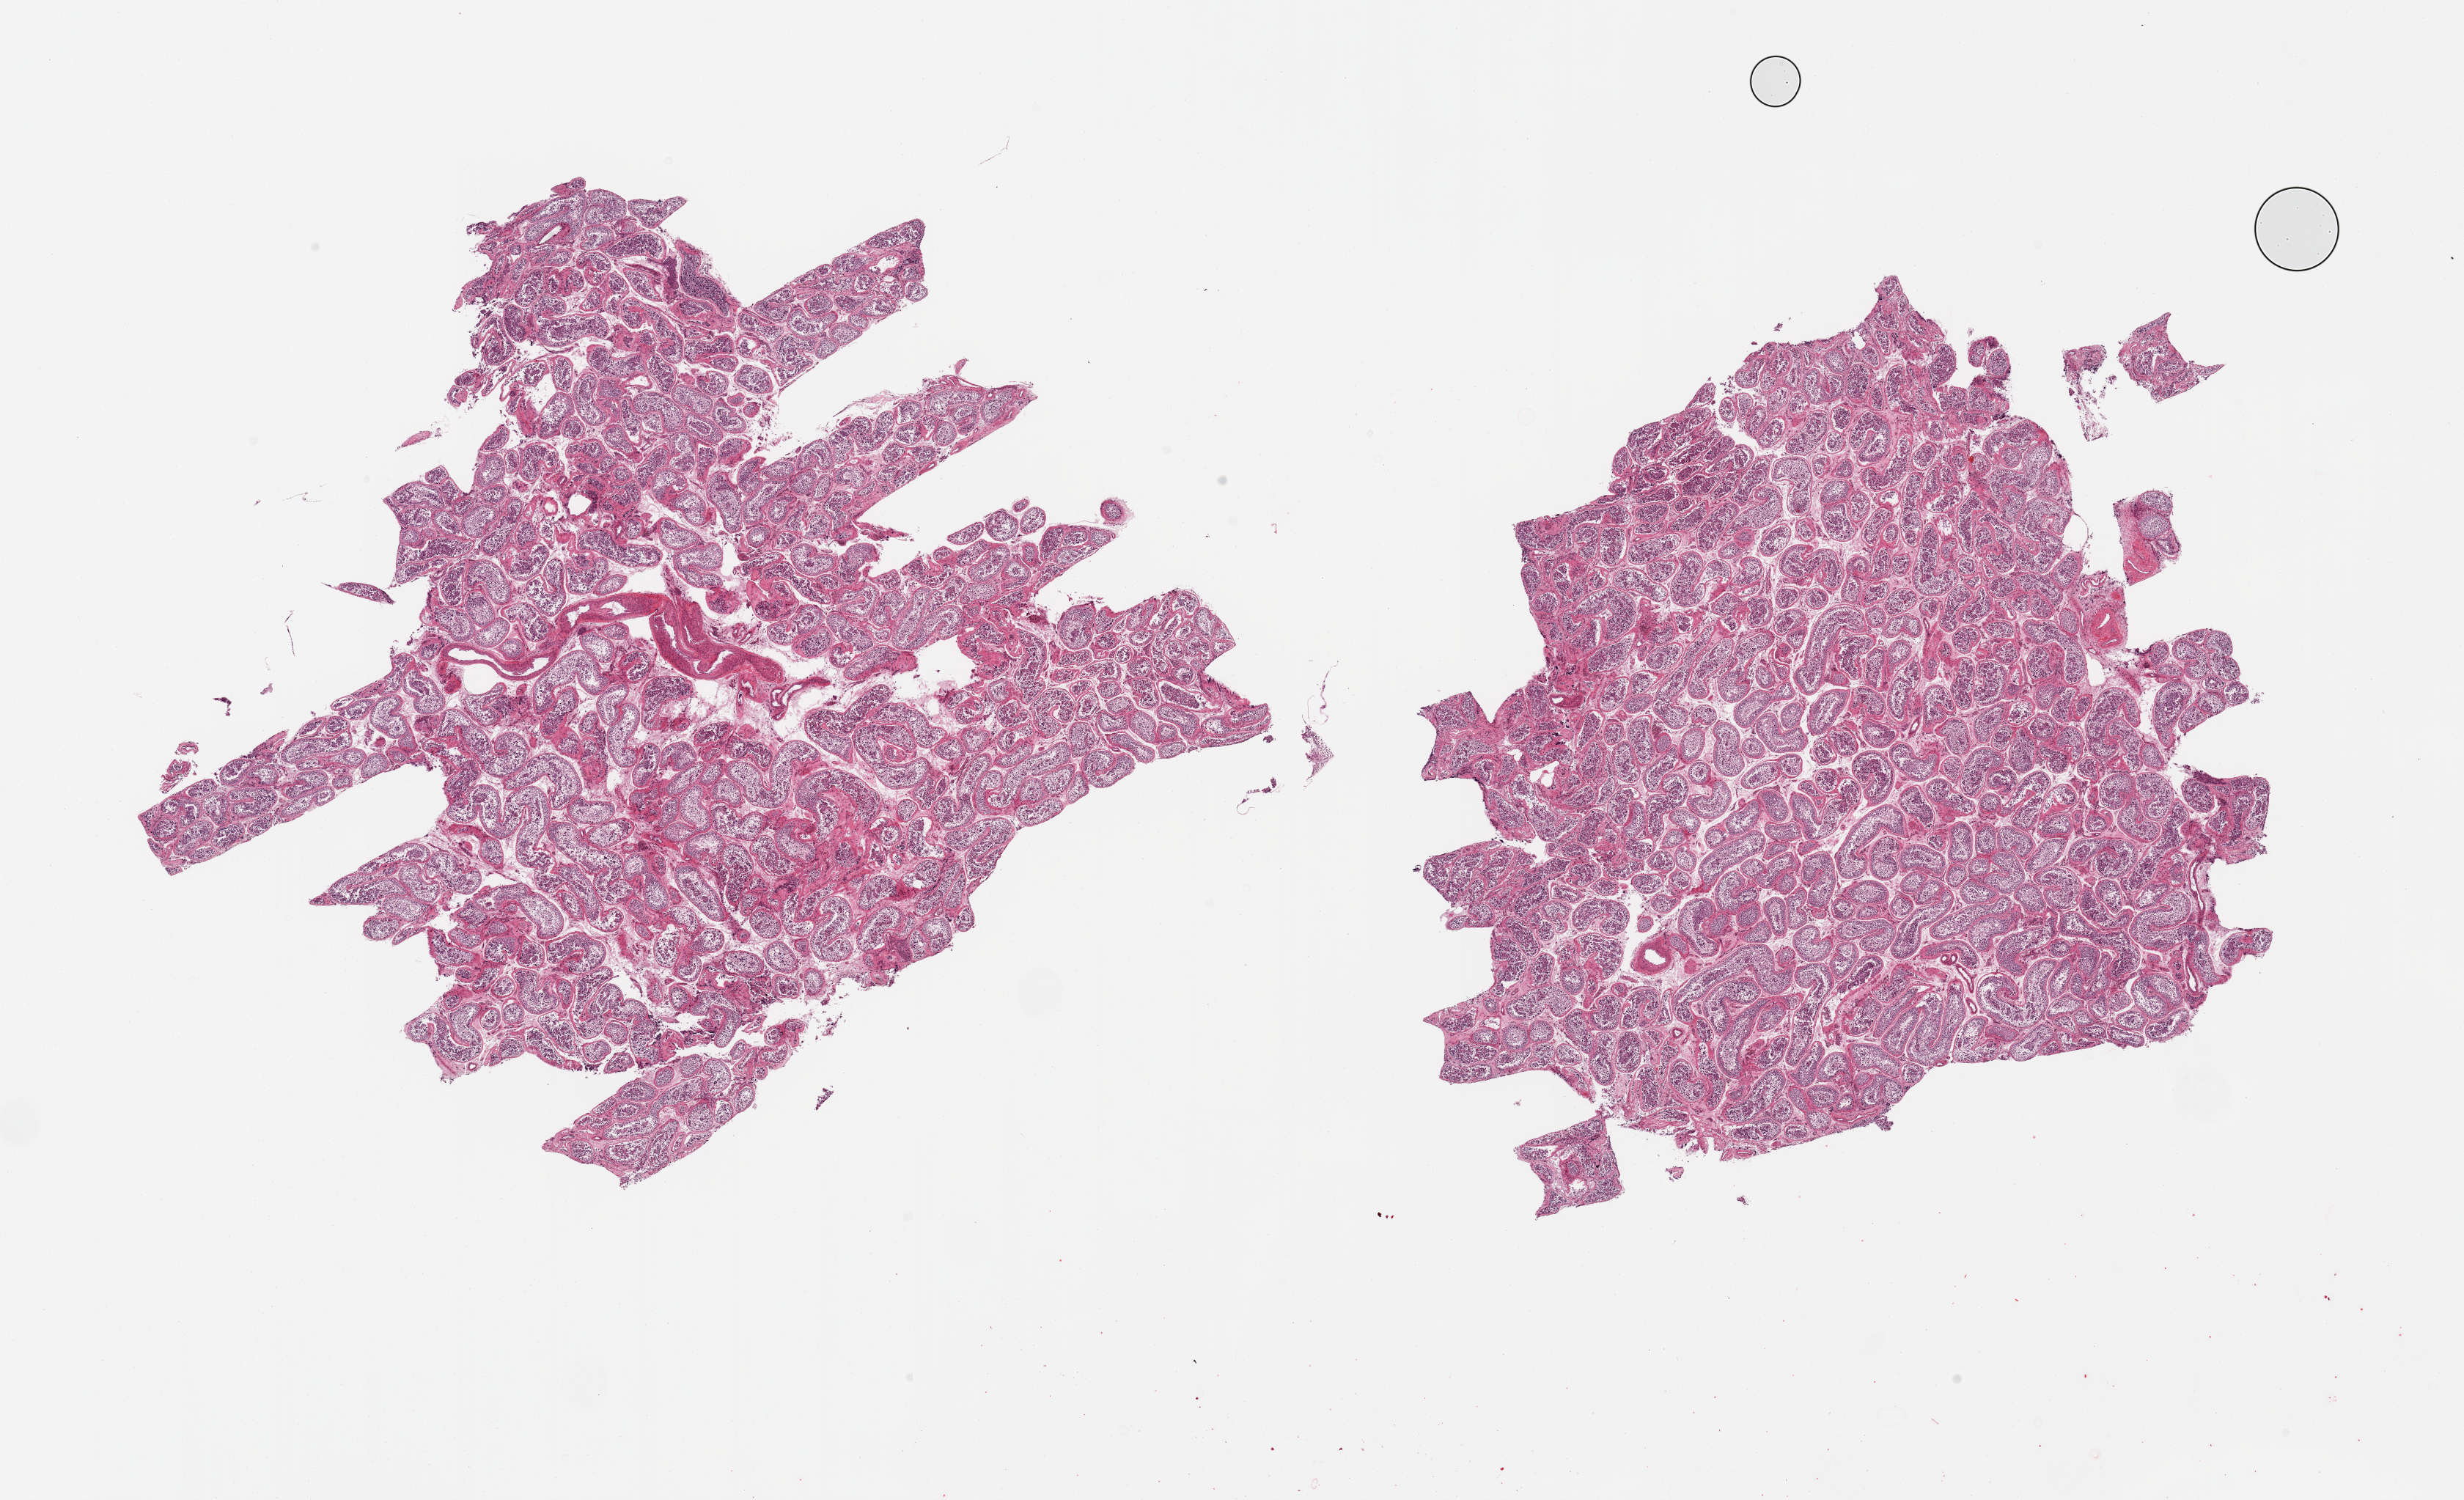
Hematoxylin and eosin (H&E) whole-slide image — whole scanned area (about 26.6 x 16.2 mm) shown as a low-resolution overview, PAXgene-fixed paraffin-embedded (PFPE) section, sampled site (target tissue): testis, tissue donor sample. Donor: male.
Reviewer comment on this tissue sample: 2 pieces, spermatogenesis is present & appears normal.